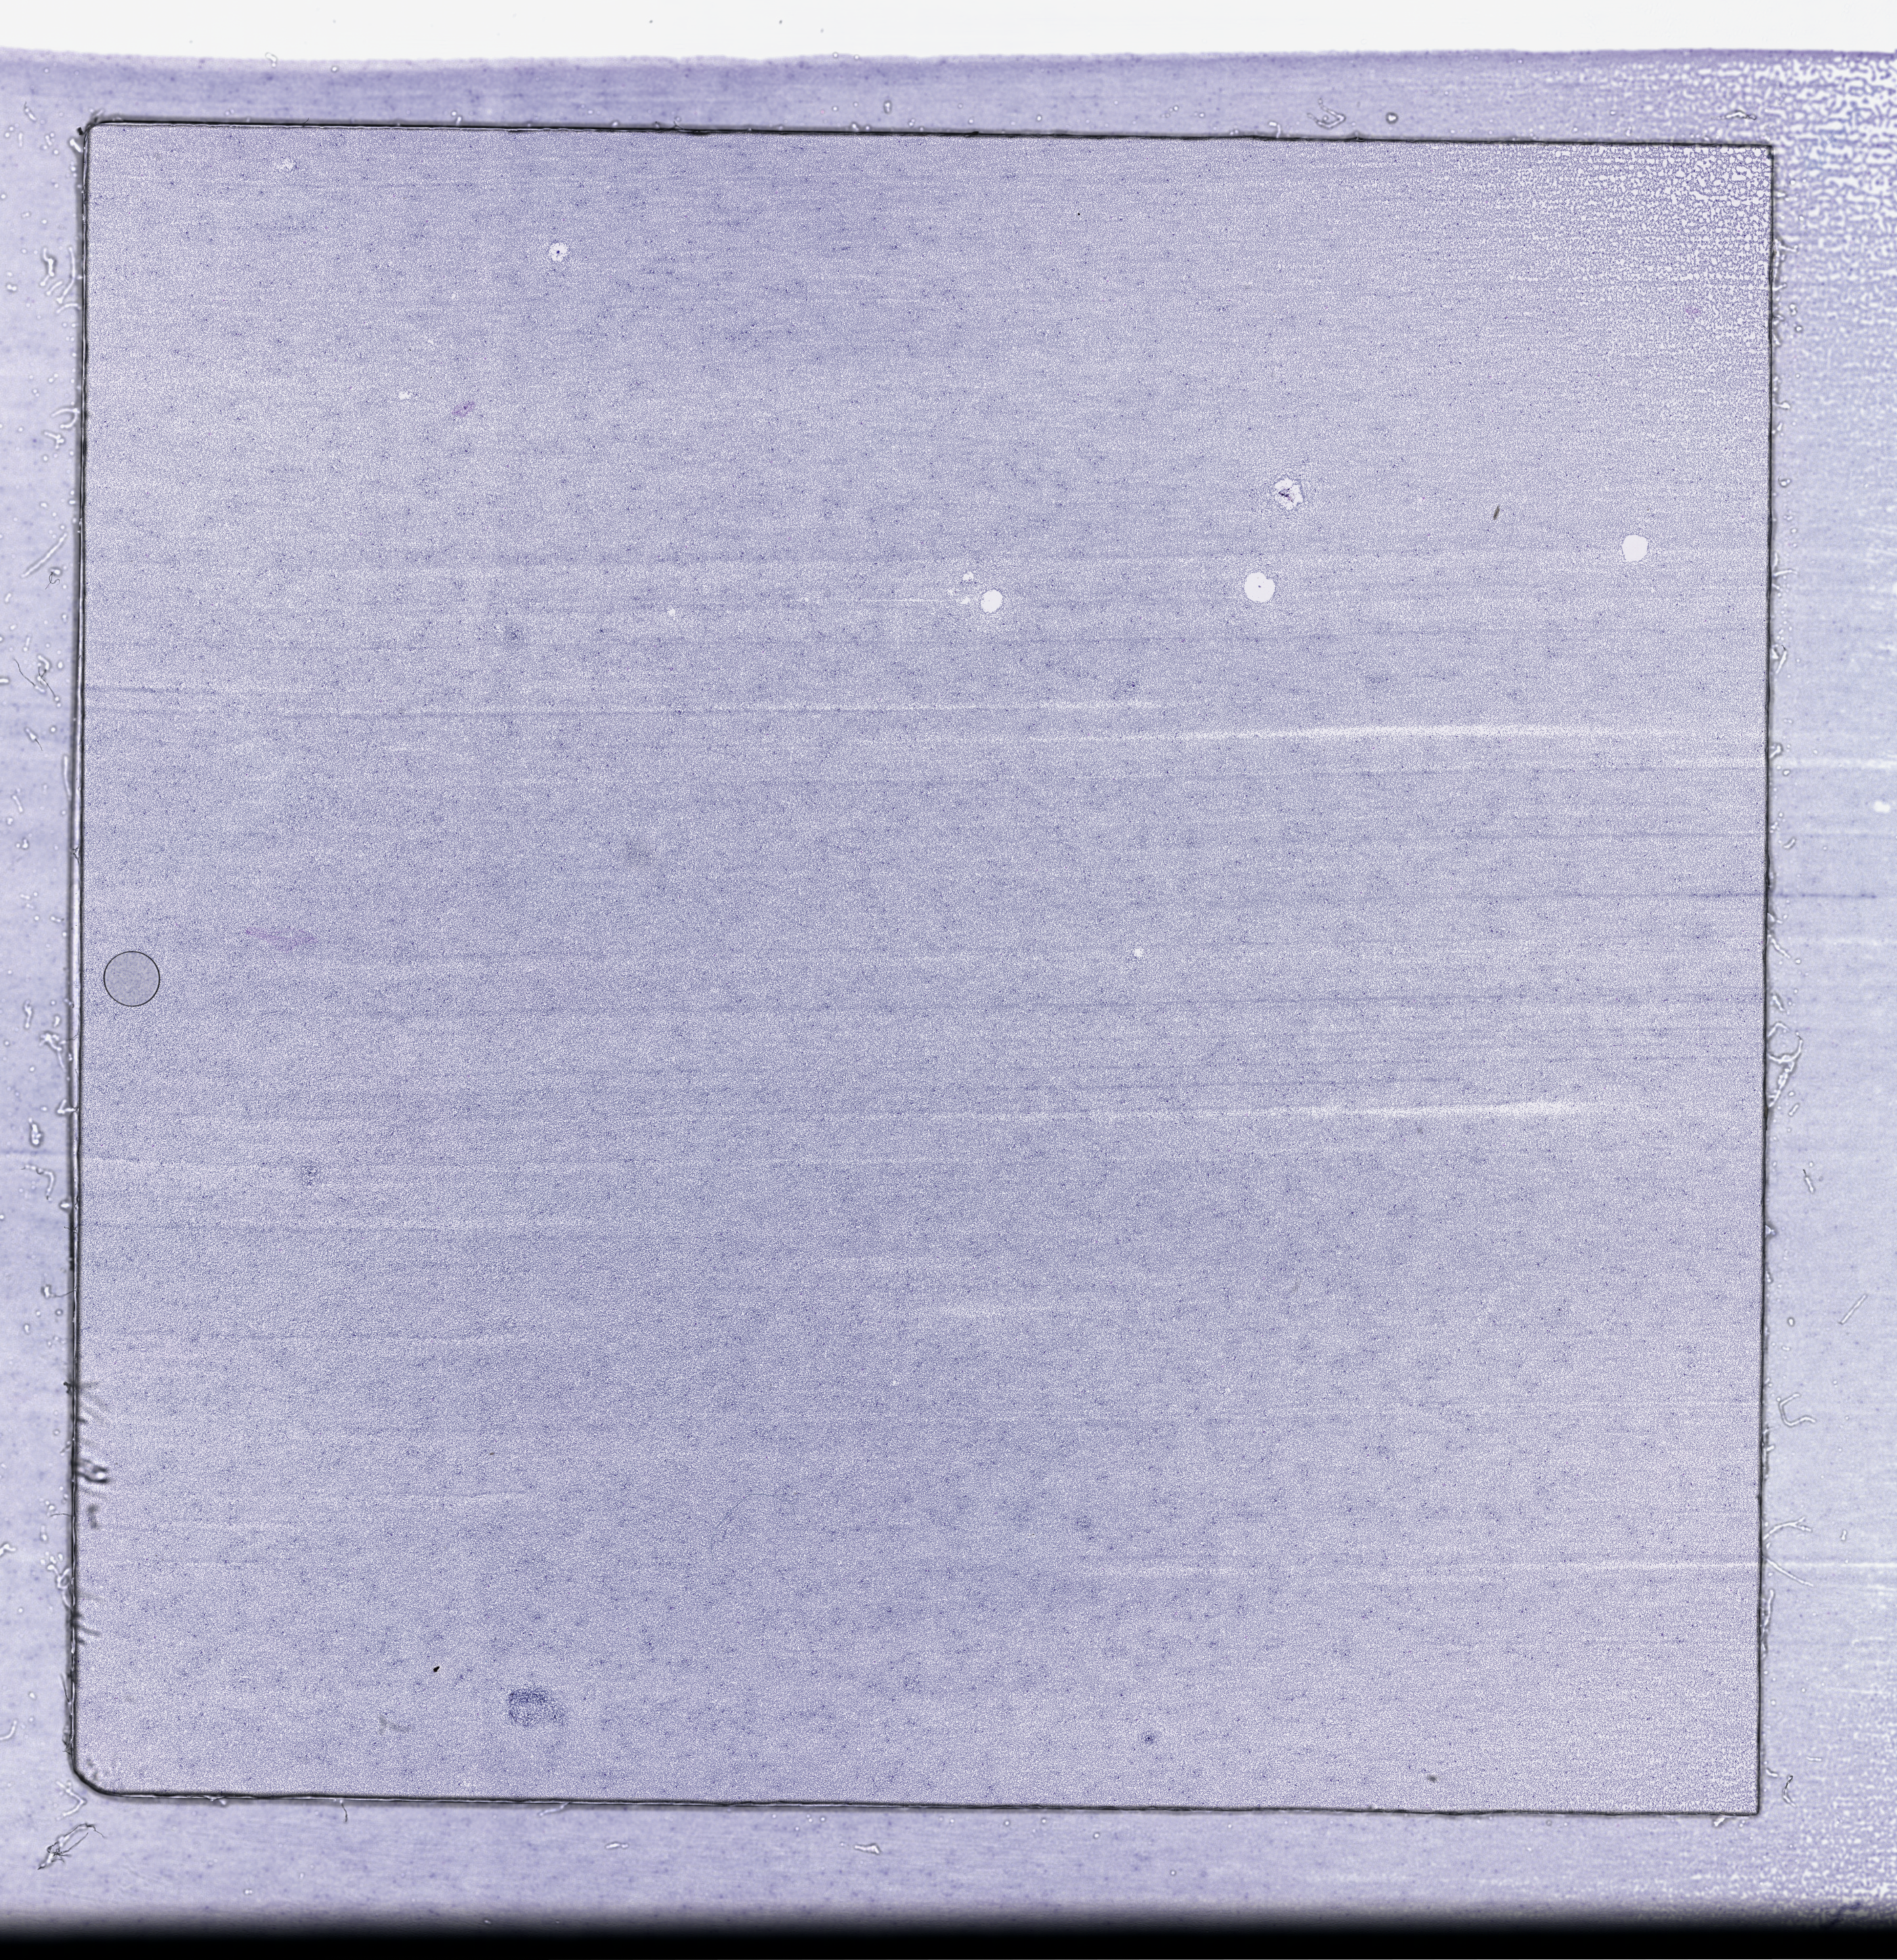
Digitized H&E-stained tissue section (whole slide), low-resolution overview of the scanned area, about 22.6 x 23.4 mm (from a 40x scan); peripheral blood (leukaemic) sample. Patient: male, age 73 years.
* diagnosis: Acute Myeloid Leukemia
* WHO classification: AML with maturation
* FAB classification: M2